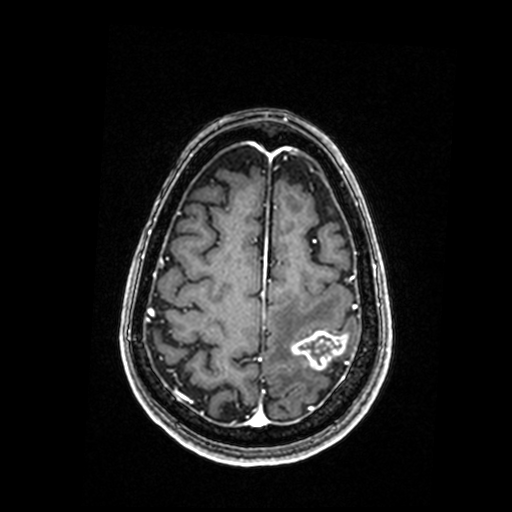
Brain MRI from a brain-tumour surgery series, one axial slice; T1-weighted post-contrast; 0.98 mm slice thickness; 512 × 512 image matrix. Case-level facts recorded for this patient, not image findings: histopathology: Metastastic Carcinoma, Poorly Differentiated; tumour location: Left Parietal.
Outlined on this slice (manually delineated by an expert):
- tumour: bounding box (x1, y1, x2, y2) in pixels: (292, 331, 347, 370)